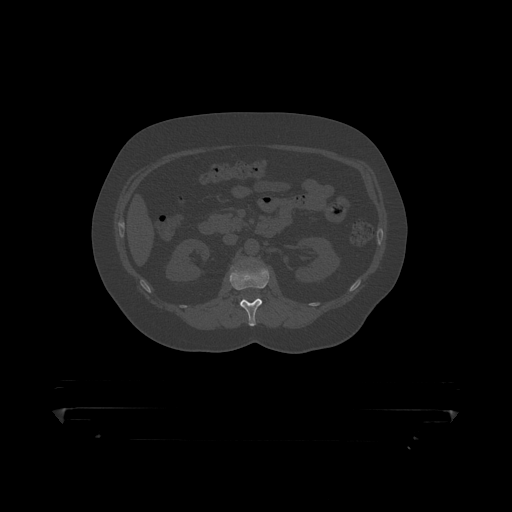
CT including the spine, one axial slice. Slice 136 of 390 in the series (ordered by position). 120 kVp. Bone window (W 1800 / L 400 HU). 512 × 512 image matrix, field of view 650 × 650 mm. Patient: male, 60 years. From the clinical record (not read from this slice): primary cancer: prostate.
Outlined on this slice (semi-automatically segmented with operator editing):
- L1 vertebra: bounding box [x1, y1, x2, y2] px = [230, 264, 270, 319]